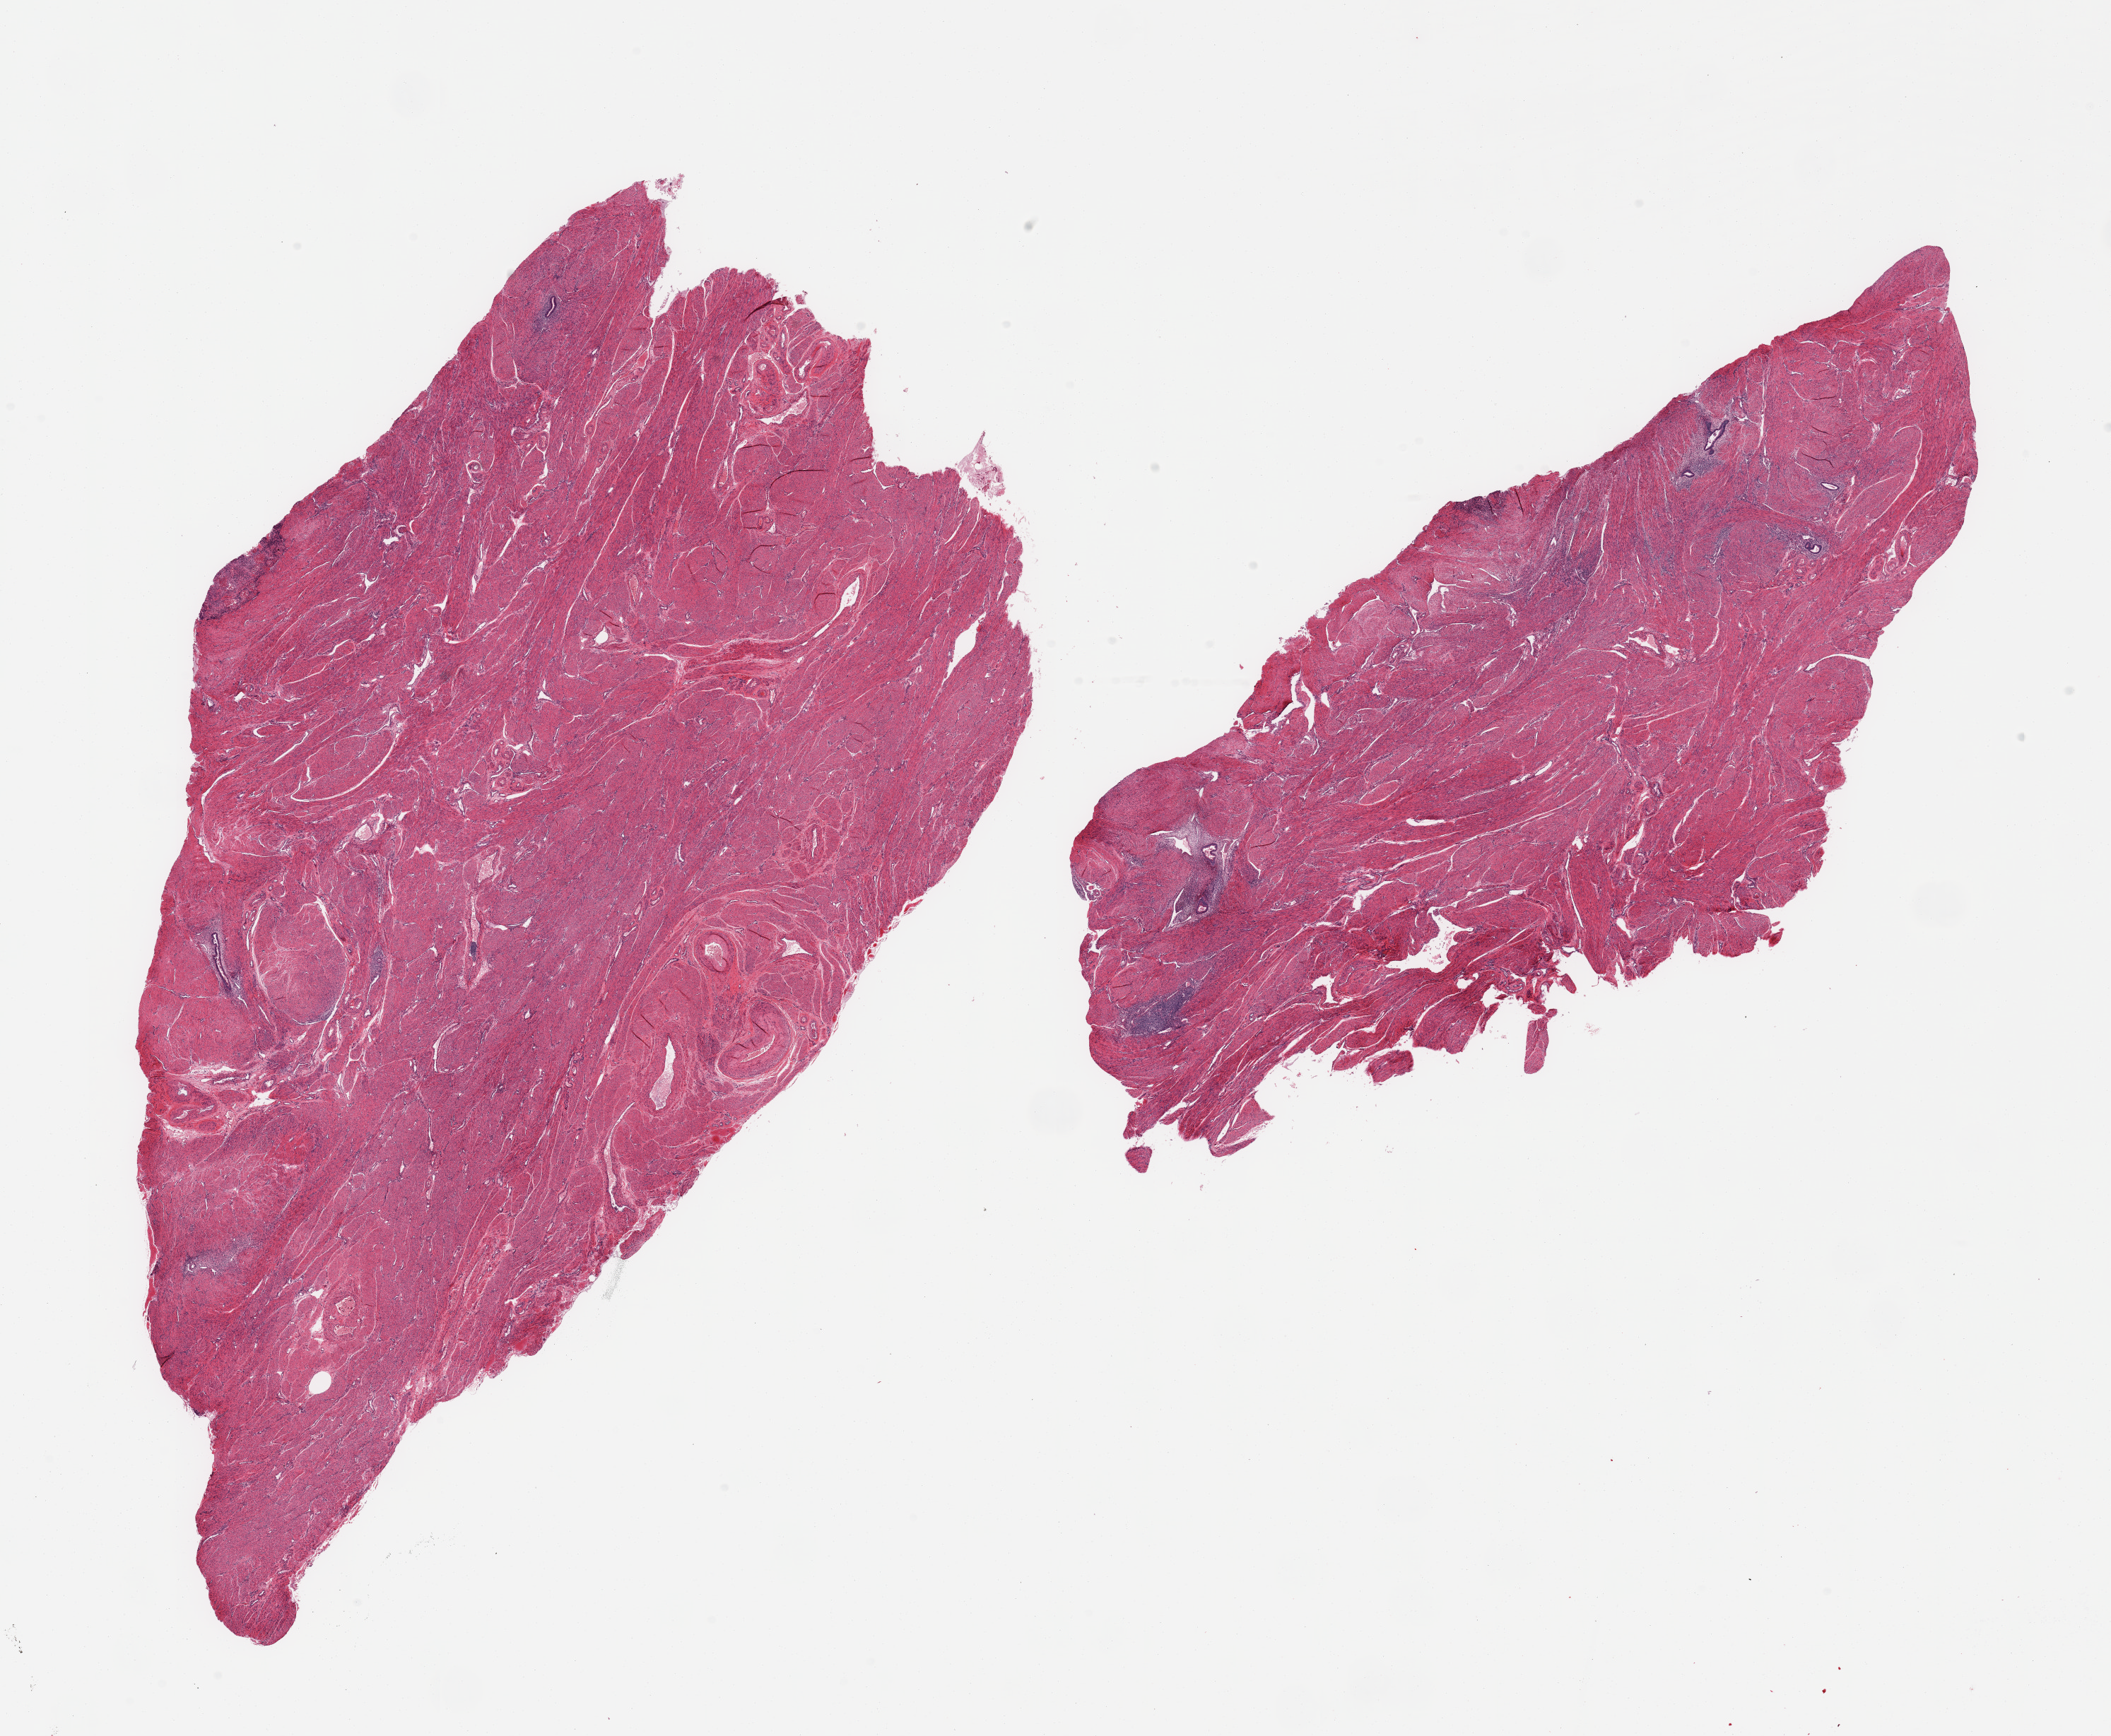
Whole-slide image, haematoxylin and eosin stain, brightfield — low-resolution overview of the scanned area, about 23.6 x 19.4 mm (acquisition: 20x scan), PAXgene-fixed, paraffin-embedded tissue, sampled site (target tissue): uterus, donor tissue sample. Donor: female.
Reviewer comment on this tissue sample: 2 pieces; myometrium and foci of endometrial glands.